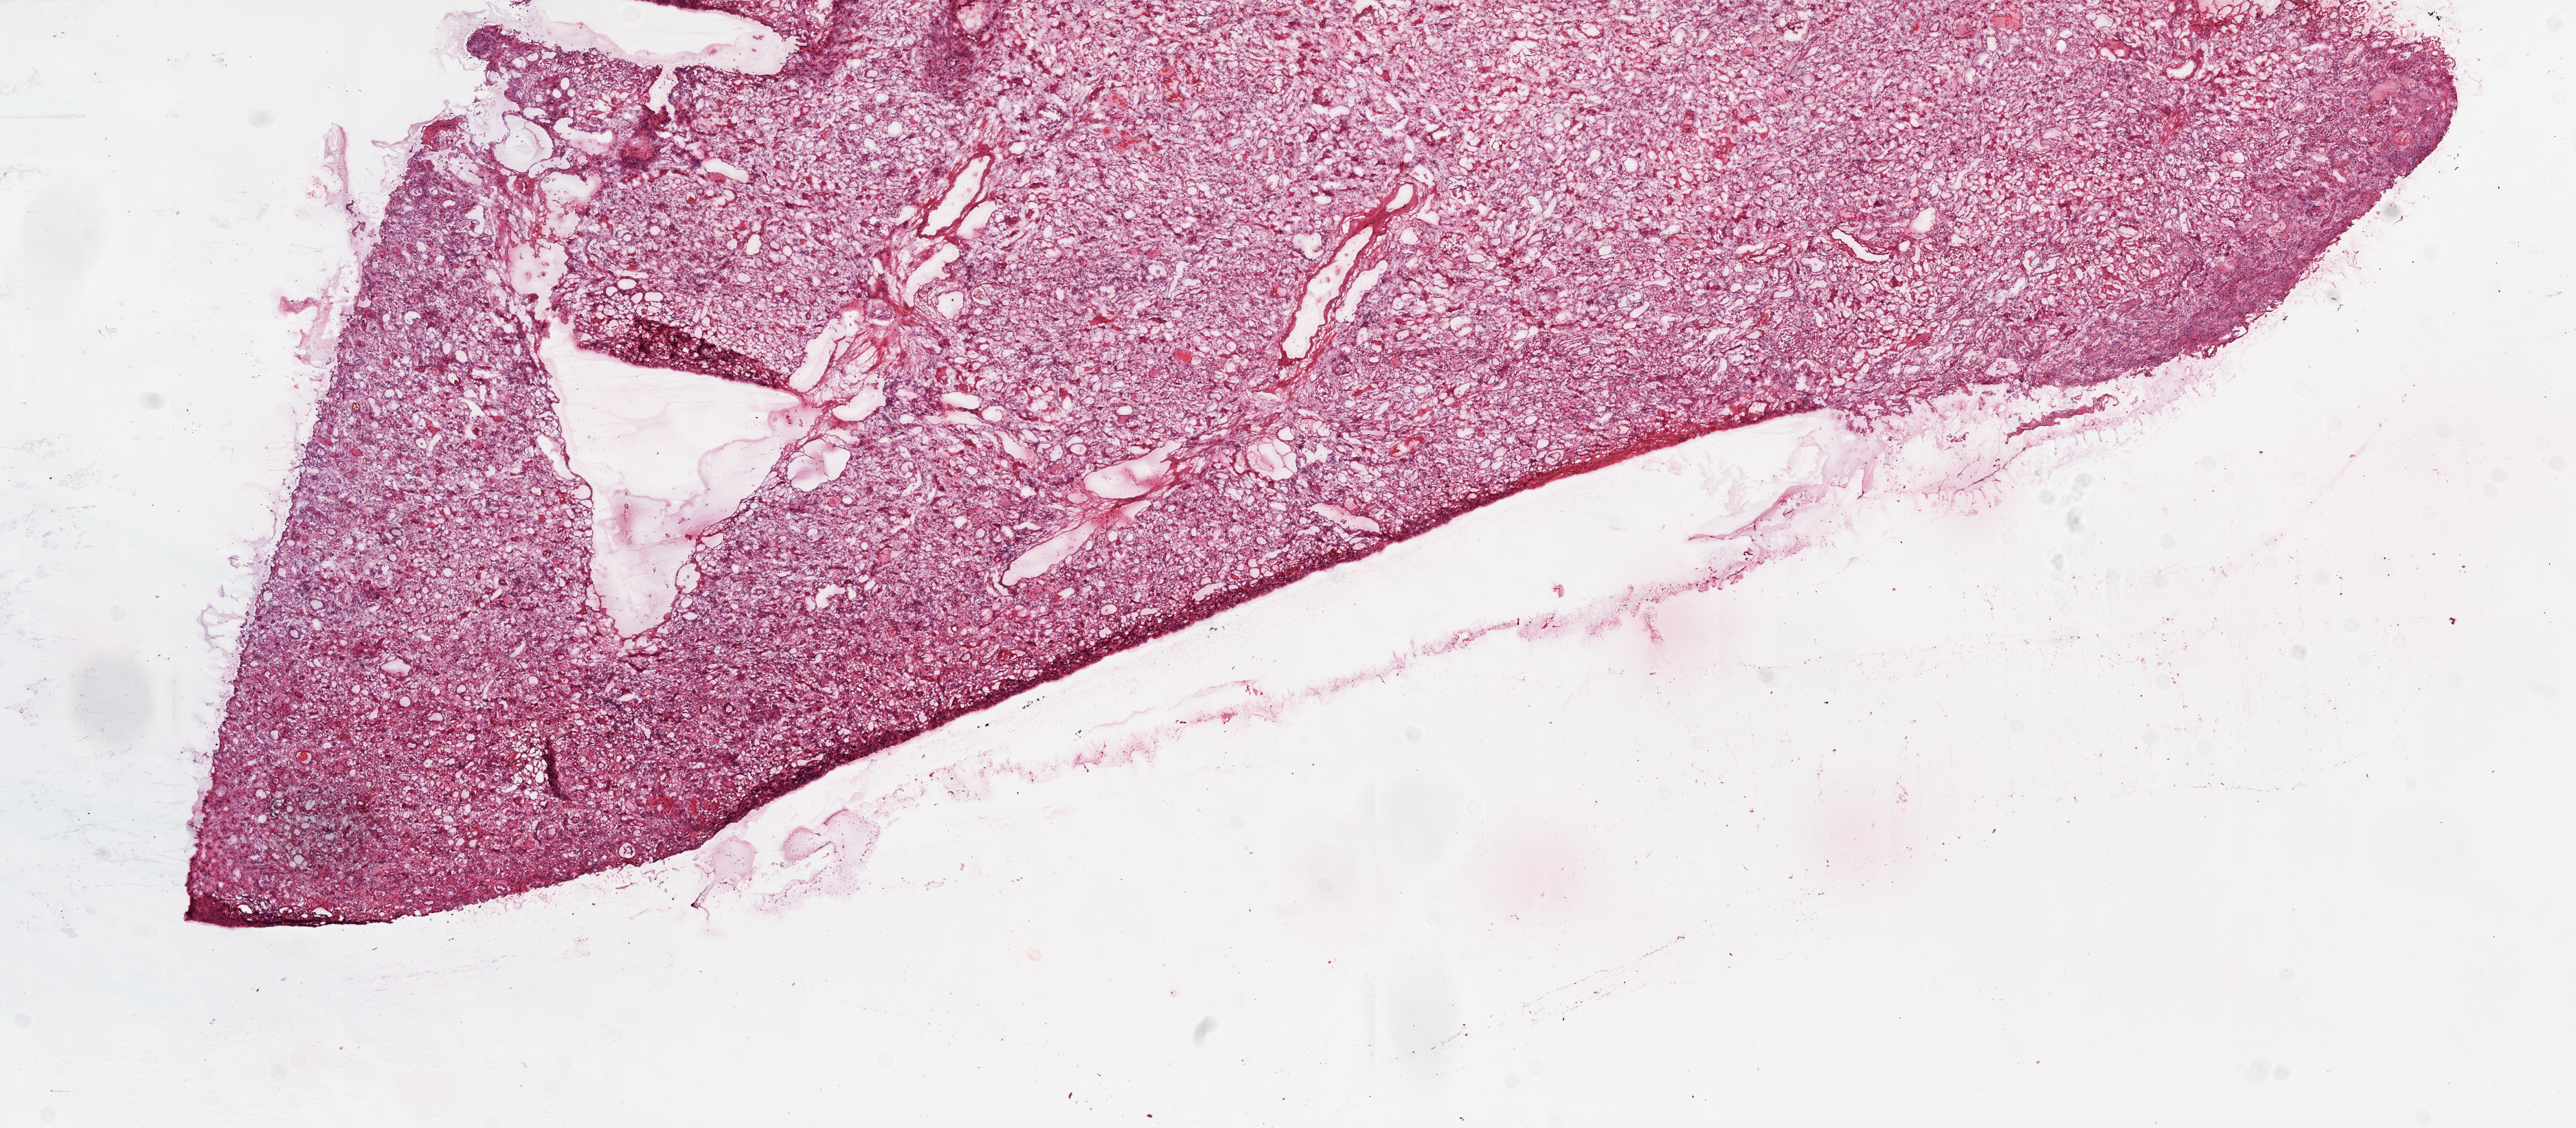
H&E whole-slide image — shown as a low-resolution overview of the whole scanned area (about 15.0 x 6.6 mm, acquisition: 20x scan), frozen section from the top of the tissue portion, solid tissue normal (non-tumour tissue) sample from the kidney. Patient: male, age at initial diagnosis 69 years.
• this section: solid tissue normal (non-tumour) sample from the same patient
• patient diagnosis: Clear cell adenocarcinoma, NOS